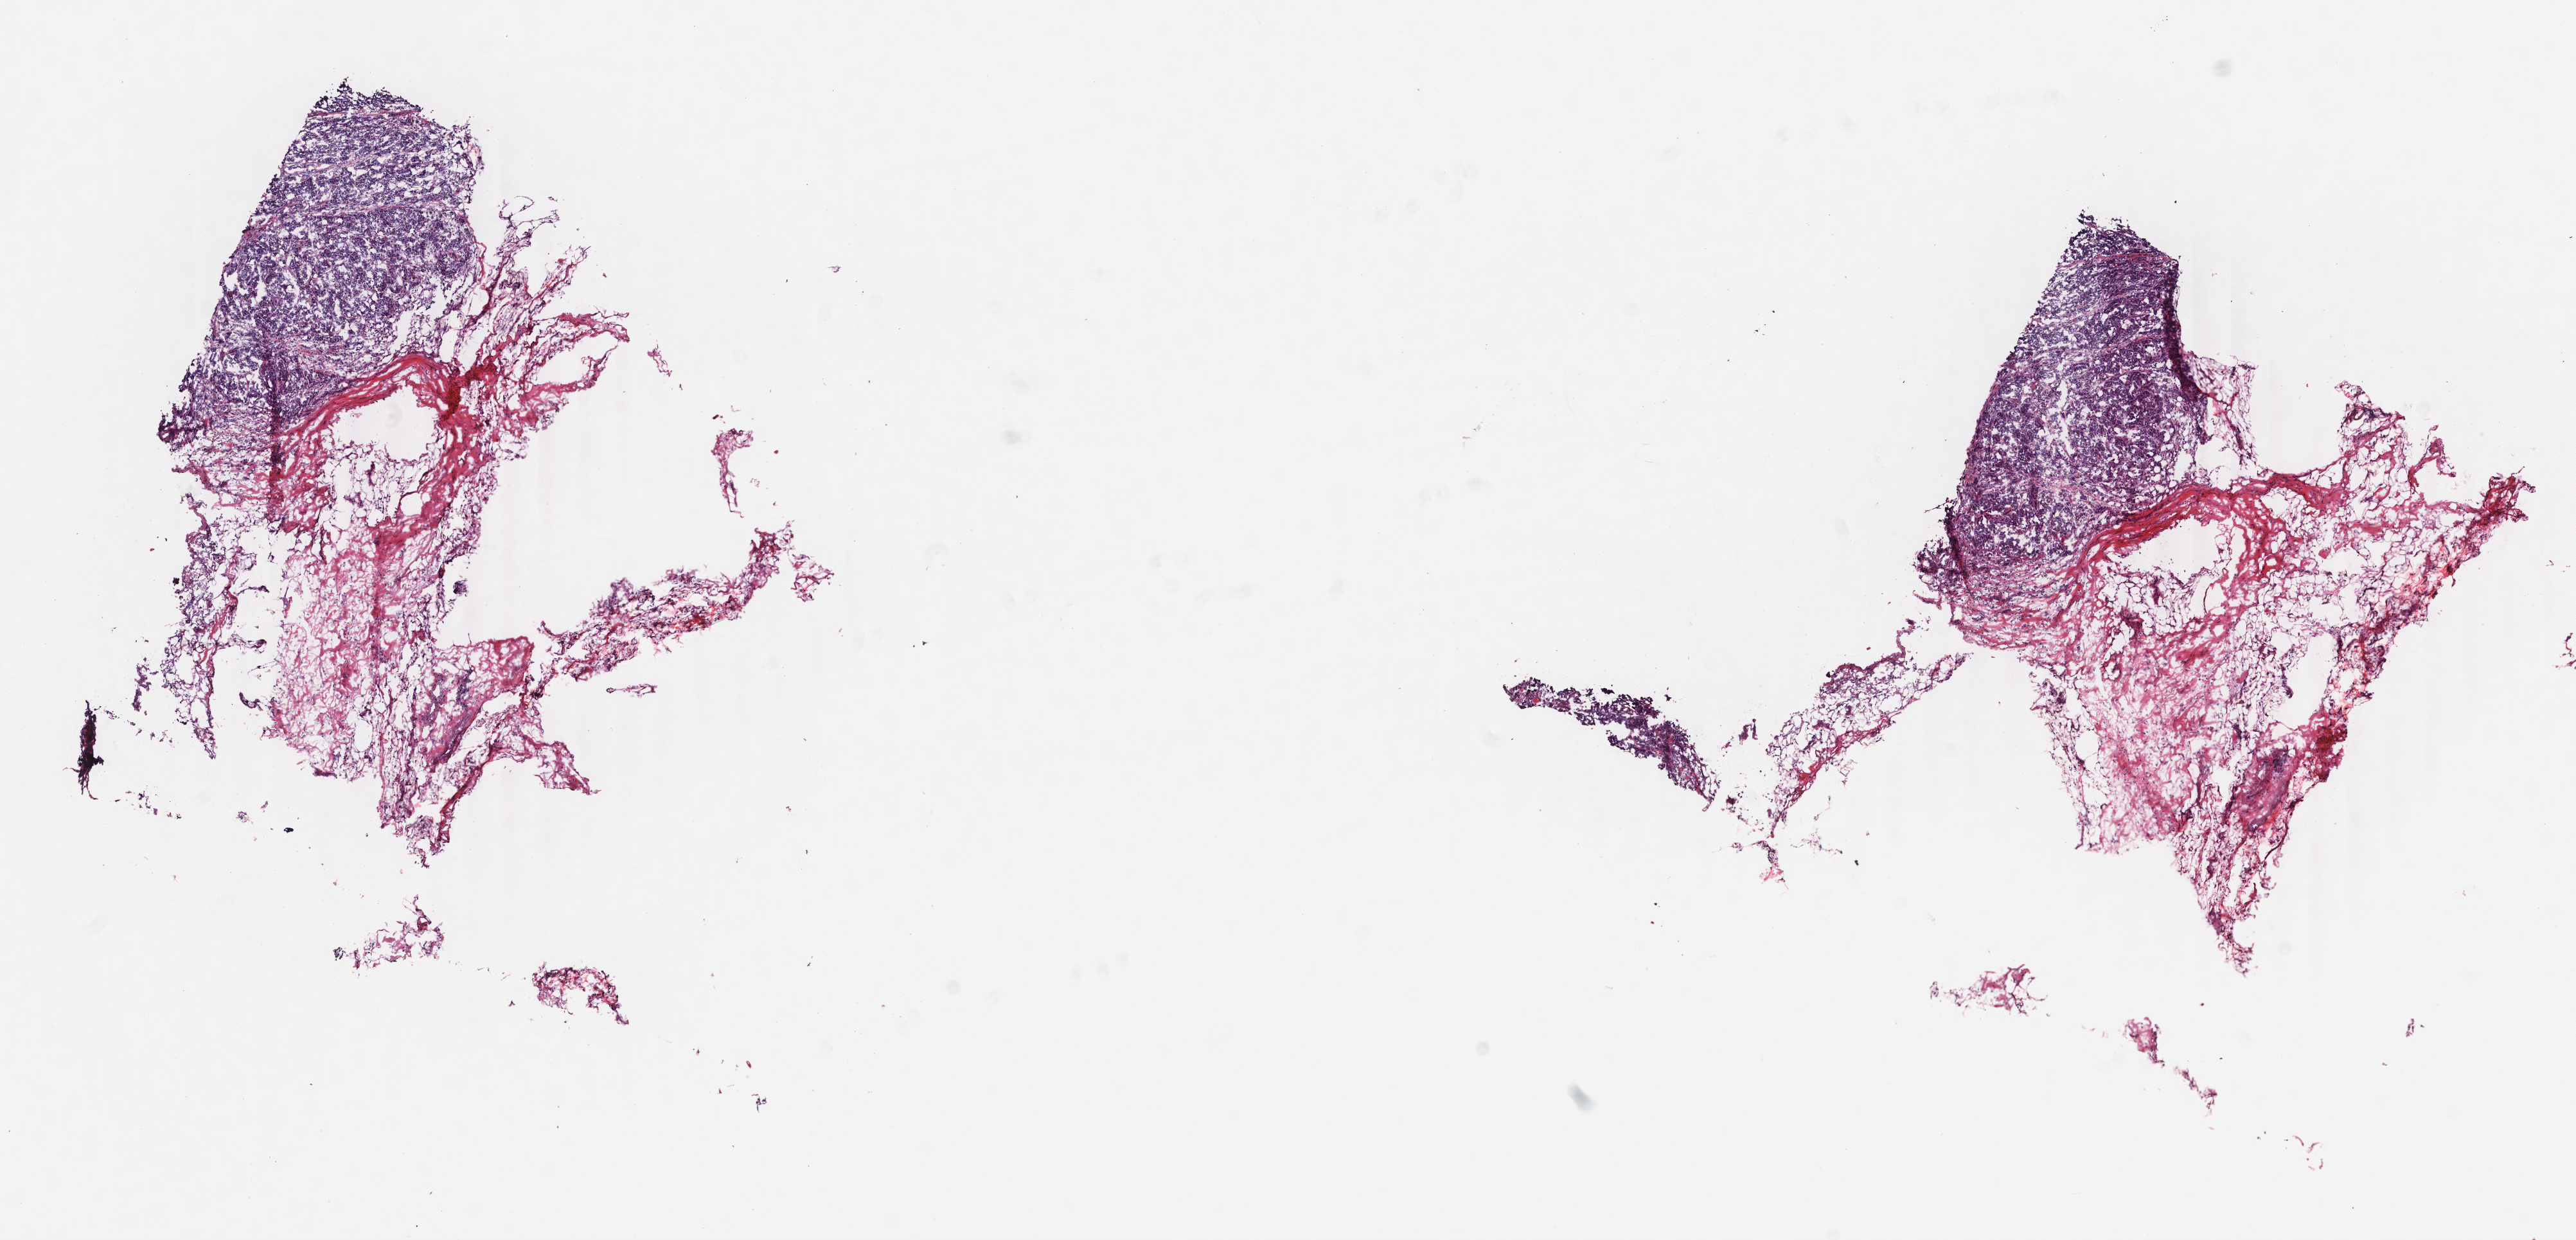
Whole-slide histology image, H&E, a low-resolution overview of the entire scanned area, about 15.9 x 7.7 mm. Frozen section from the bottom of the tissue portion. Breast, primary tumour sample. Female, age 67 years at initial diagnosis. Composition of this section per pathologist review: tumour cells 30%, tumour nuclei 85%, normal cells 0%, stromal cells 70%, necrosis 0%. Inflammatory infiltration, as recorded: lymphocyte infiltration 0%, monocyte infiltration 0%, neutrophil infiltration 0%.
• pathologic diagnosis: Infiltrating duct carcinoma, NOS
• laterality: left
• AJCC pathologic stage: IIA
• lymph nodes positive (case pathology): 0 of 5 examined